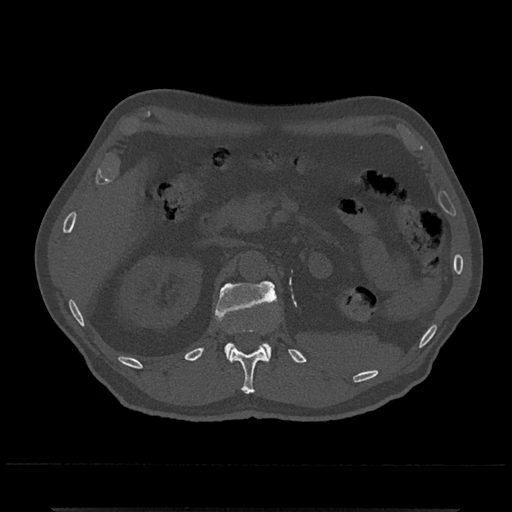
CT including the spine, one axial slice; slice 401 of 797 in the series (ordered by position); 120 kVp; bone window (W 1800 / L 400 HU); 0.5 mm slice thickness; 512 × 512 image matrix, field of view 393 × 393 mm. Male patient, age 67 years. From the clinical record (not read from this slice): primary cancer: prostate.
Structures marked on this image (semi-automatic segmentation, software-assisted and operator-edited):
- L1 vertebra: bounding box (x1, y1, x2, y2) in pixels: (215, 281, 277, 361)
- T12 vertebra: (230, 329, 269, 394)